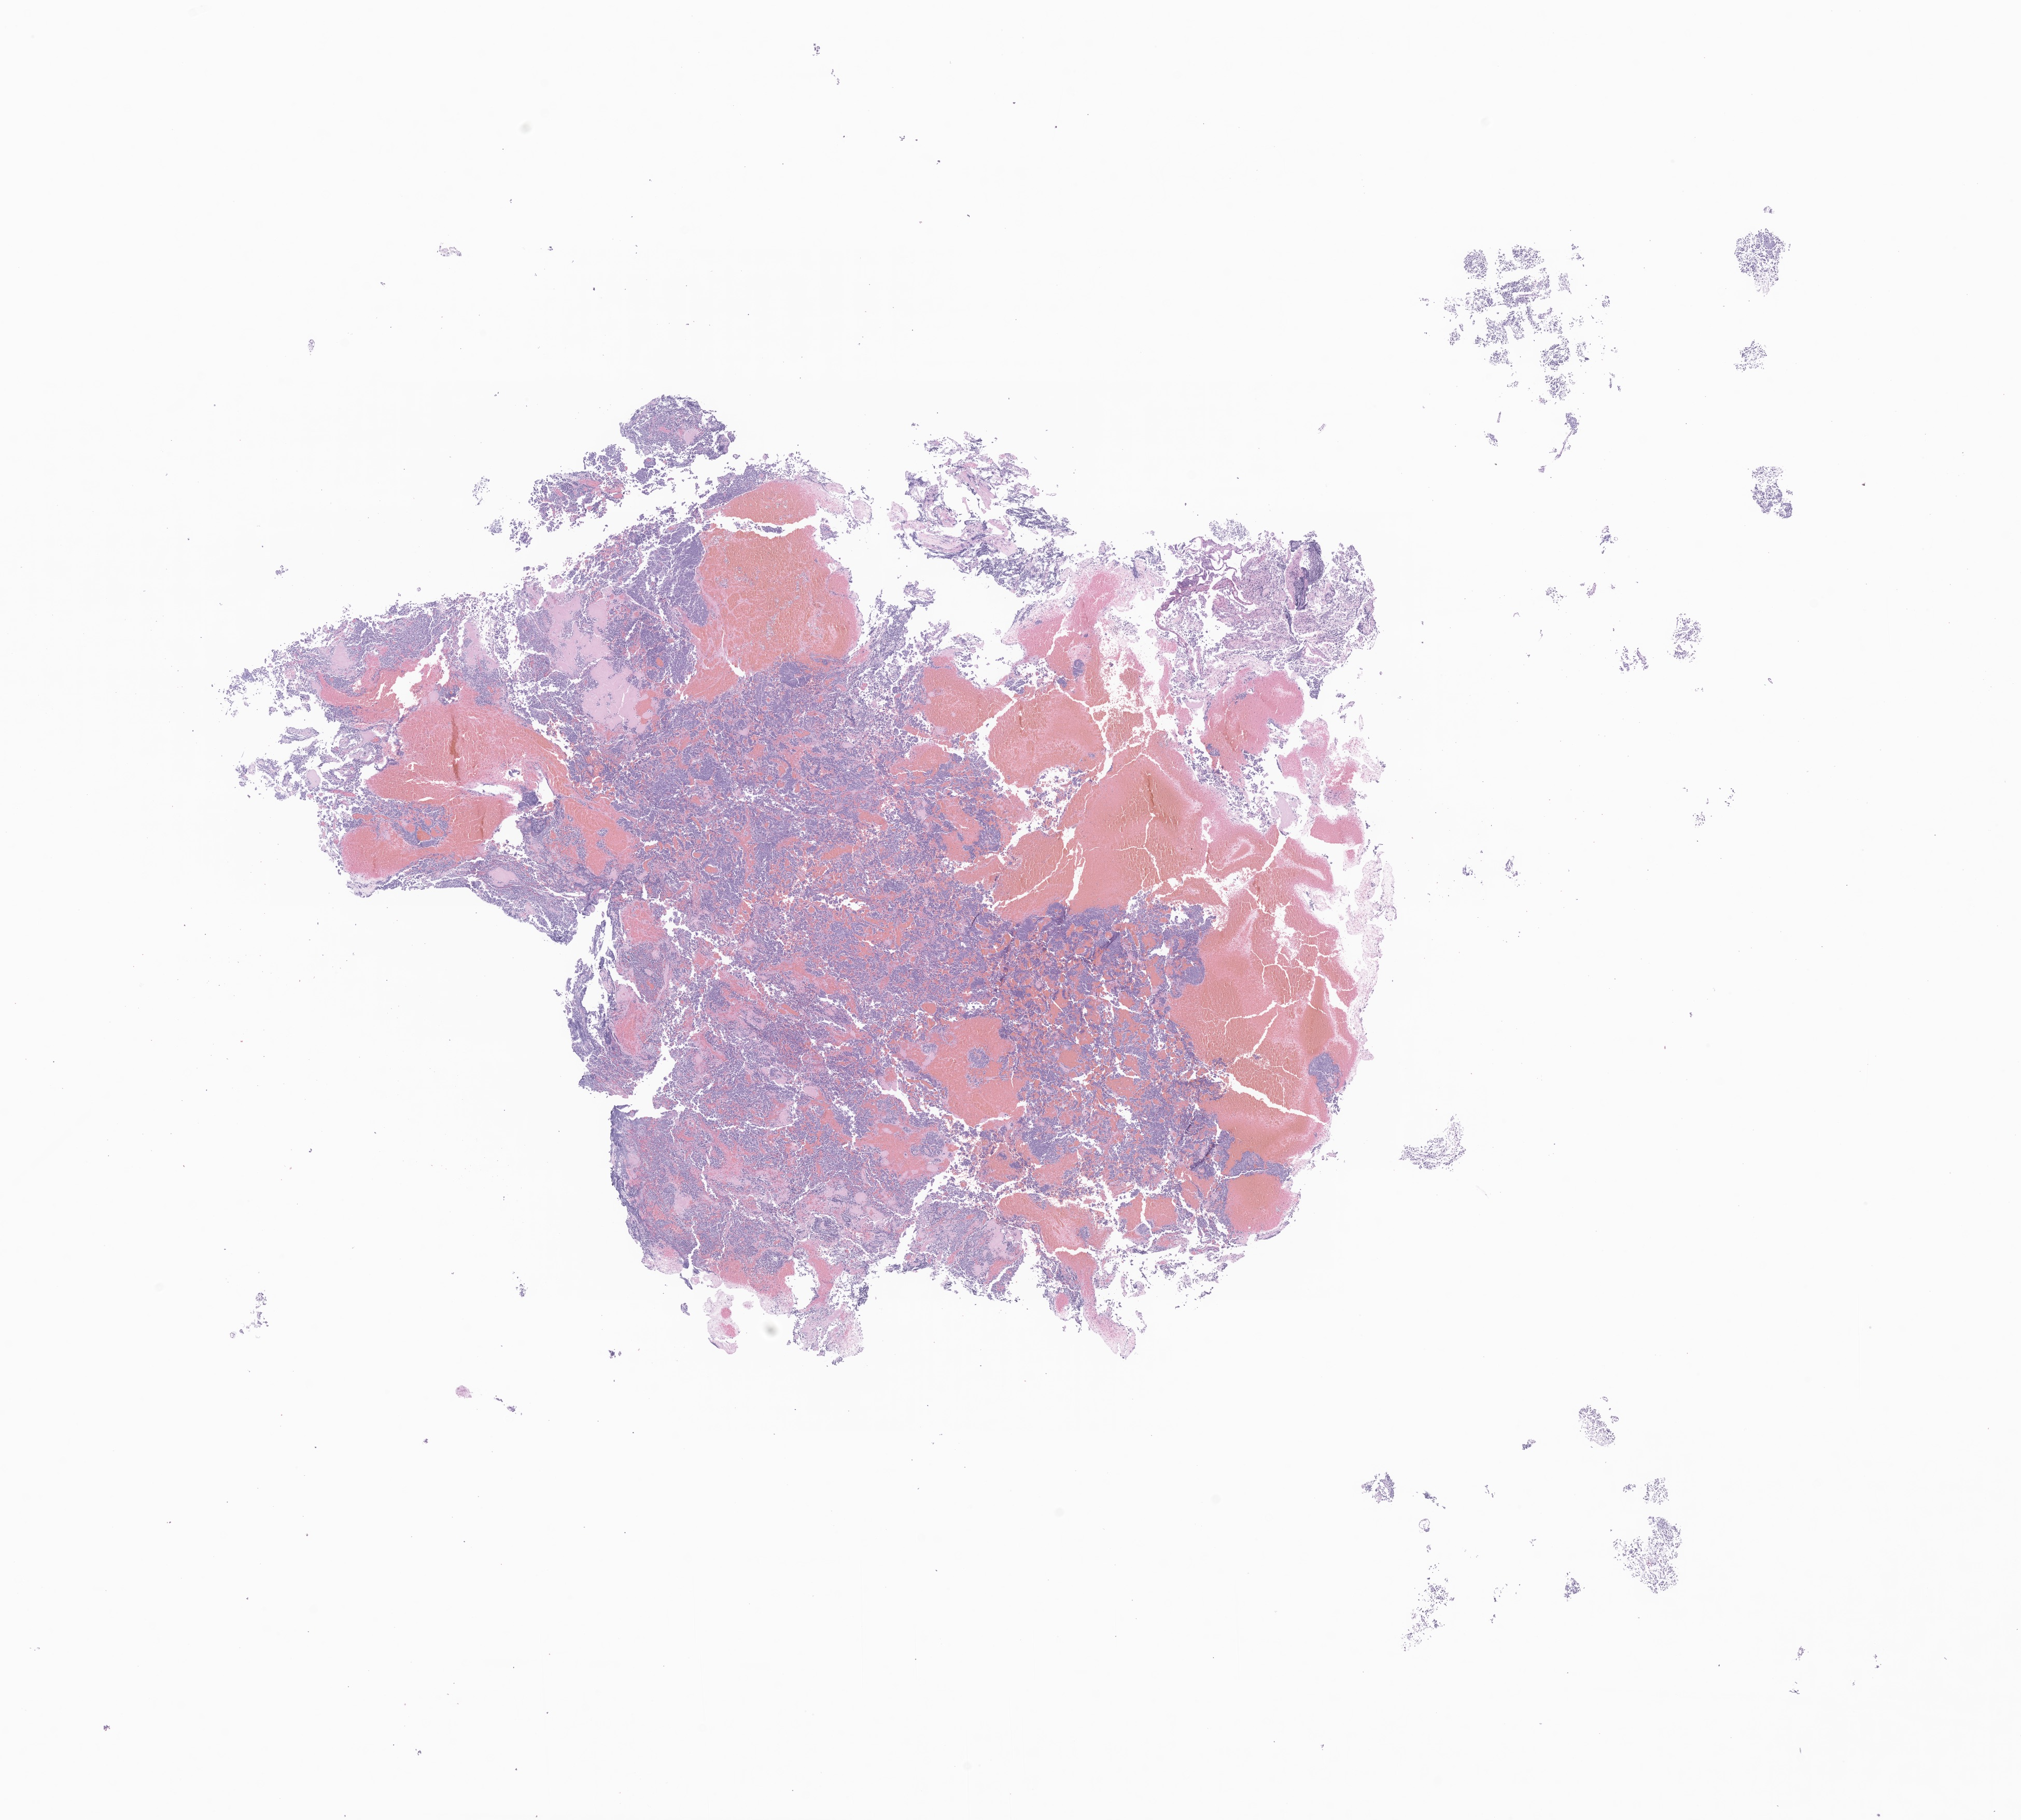
Whole-slide image, hematoxylin and eosin (H&E) stain of tumor tissue from the brain stem — a low-resolution overview of the entire scanned area, about 16.4 x 14.8 mm; formalin-fixed, paraffin-embedded (FFPE) tissue. Female patient, age 791 days.
Diagnosis (ICD-O-3 morphology term): Medulloblastoma, NOS.